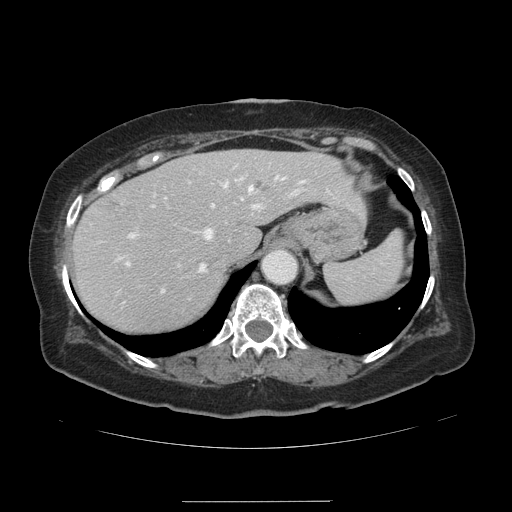
Contrast-enhanced abdominal CT, one axial slice; slice 100 of 141 in the series (ordered by position); intravenous contrast given; soft-tissue window (W 400 / L 40 HU); 512 × 512 image matrix, field of view 393 × 393 mm. Female patient, age 74 years. Case-level facts recorded for this patient, not image findings: diagnosis: colorectal cancer liver metastases, imaged before liver resection; multiple liver metastases: yes; largest metastasis: 7 cm; disease in both lobes: yes.
Annotated regions visible in this slice (expert manual segmentation):
- hepatic veins: bounding box <114,176,303,273> (left, top, right, bottom; pixels)
- liver: <74,150,364,335>
- planned liver remnant (the part of the liver to remain after resection): <75,150,364,335>
- portal vein (with intrahepatic branches): <127,177,299,292>
- liver metastasis: <254,180,265,191>
- liver metastasis: <101,196,121,209>